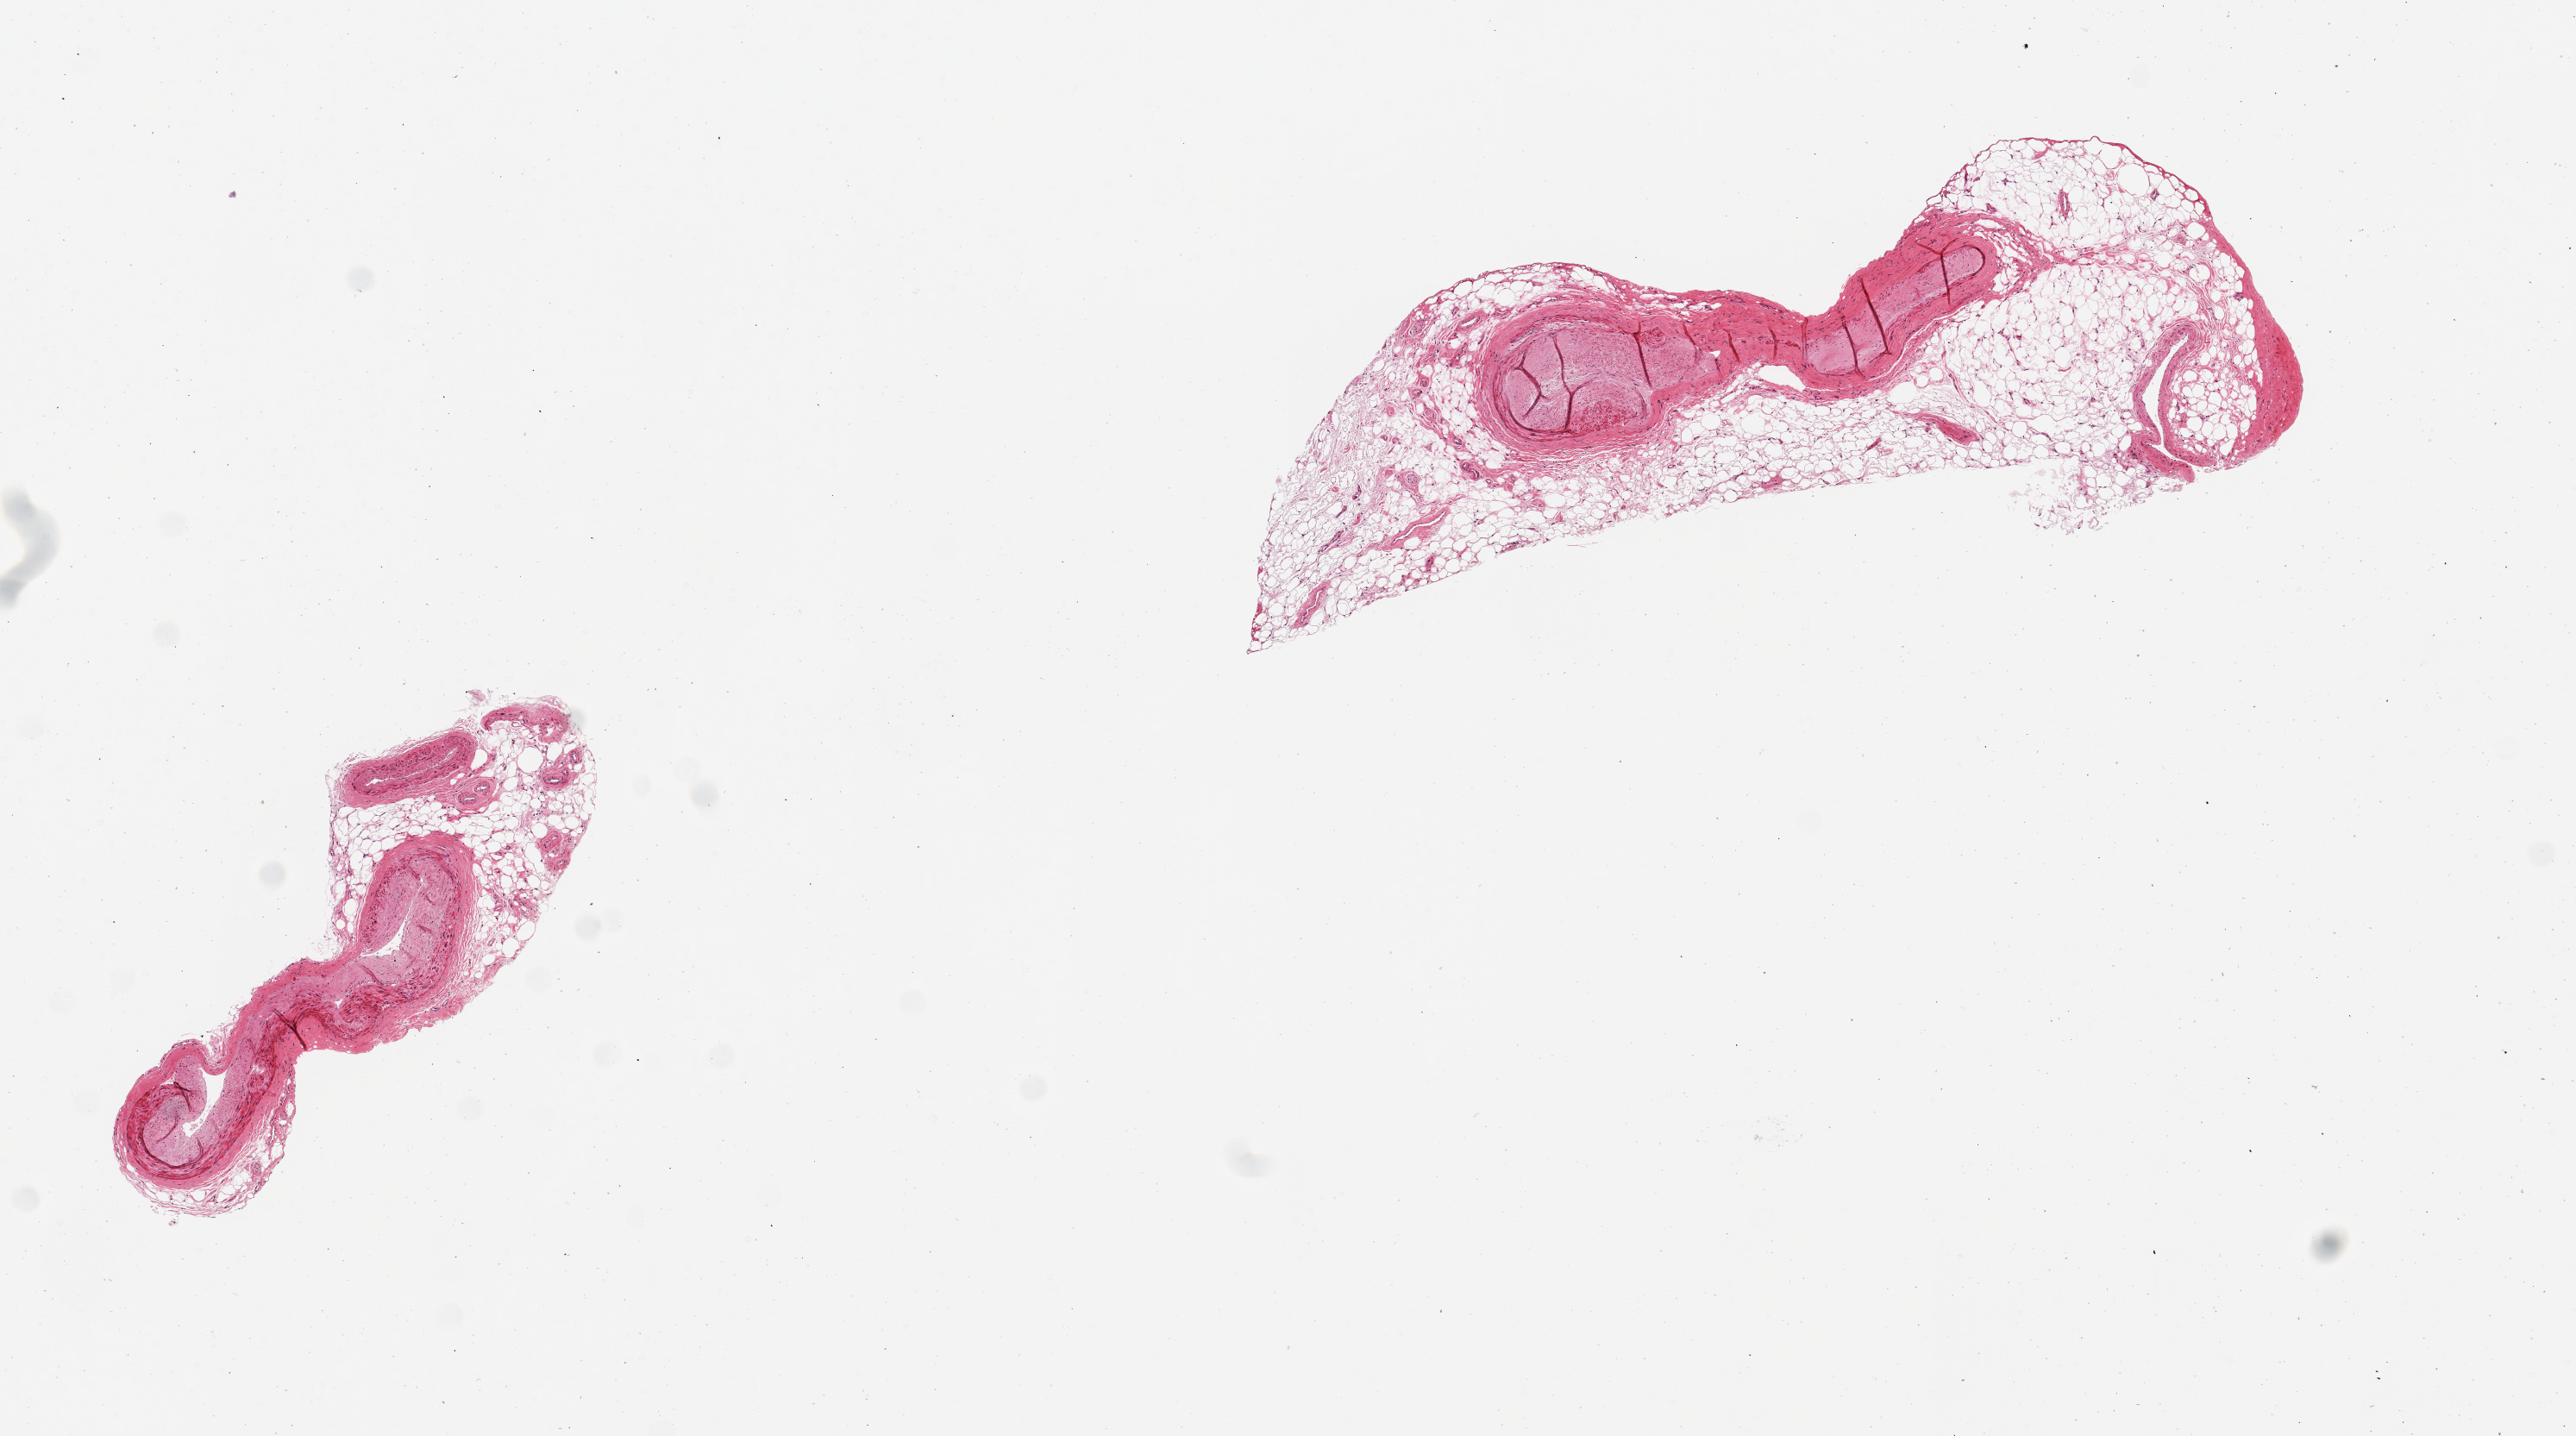
Digitized H&E-stained section, brightfield, shown as a low-resolution overview of the whole scanned area (about 11.8 x 6.6 mm, from a 20x scan). Male donor.
Specimen: PAXgene-fixed, paraffin-embedded tissue; target tissue: coronary artery; donor tissue sample.